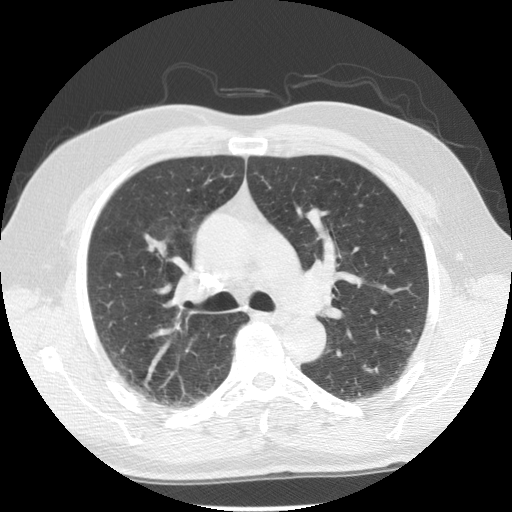
Axial slice from a low-dose chest CT screening exam, first (baseline) screen, lung window (W 1500 / L -600 HU), 2.5 mm slice thickness, standard (soft-tissue) reconstruction kernel (STANDARD). Male, age 59 years at enrolment. Current smoker at enrolment.
• Expert reader's lesion annotation, box from (x=131, y=224) to (x=173, y=264) px.
• No non-calcified nodule or mass ≥4 mm was recorded by the screening reader at this exam.